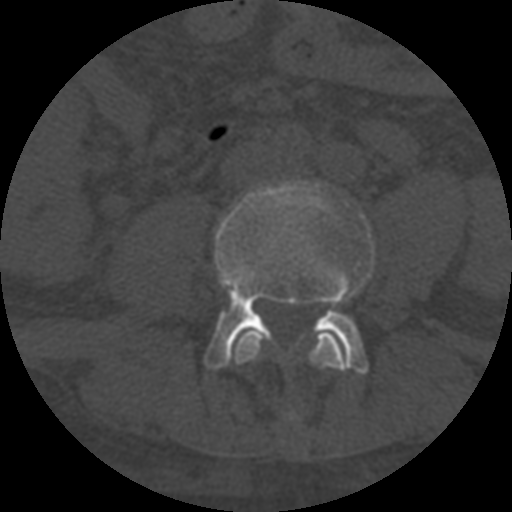
CT including the spine, one axial slice. Slice 217 of 708 in the series (ordered by position). Reconstruction kernel STANDARD. 120 kVp. One of 3 acquisitions stored at this slice position. Bone window (W 1800 / L 400 HU). 1.25 mm slice thickness. 512 × 512 image matrix. Patient age 55 years. Case-level facts recorded for this patient, not image findings: primary cancer: colon; vertebrae with lytic lesions (as recorded): T12, L1, L5.
Structures marked on this image (semi-automatic segmentation, software-assisted and operator-edited):
- L3 vertebra: bounding box <232,330,348,371> (left, top, right, bottom; pixels)
- L4 vertebra: <205,180,368,374>